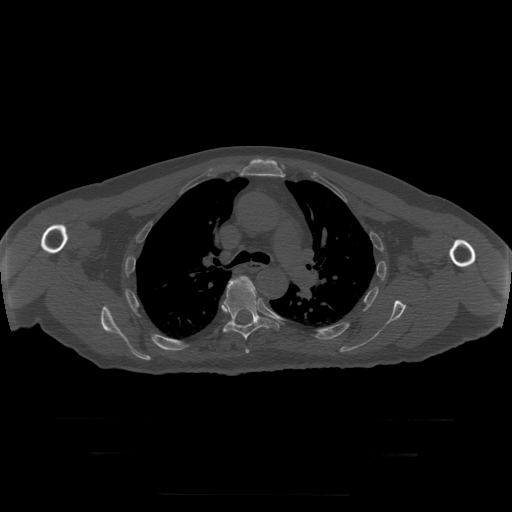
CT including the spine, one axial slice; position 210 of 397 along the scan axis; reconstruction kernel STANDARD; bone window (W 1800 / L 400 HU); 1.25 mm slice thickness; 512 × 512 image matrix, field of view 510 × 510 mm. Patient age 73 years. From the clinical record (not read from this slice): primary cancer: prostate.
Annotated regions visible in this slice (semi-automatic segmentation, software-assisted and operator-edited):
- T5 vertebra: bounding box <246,349,250,354> (left, top, right, bottom; pixels)
- T6 vertebra: <223,276,280,340>